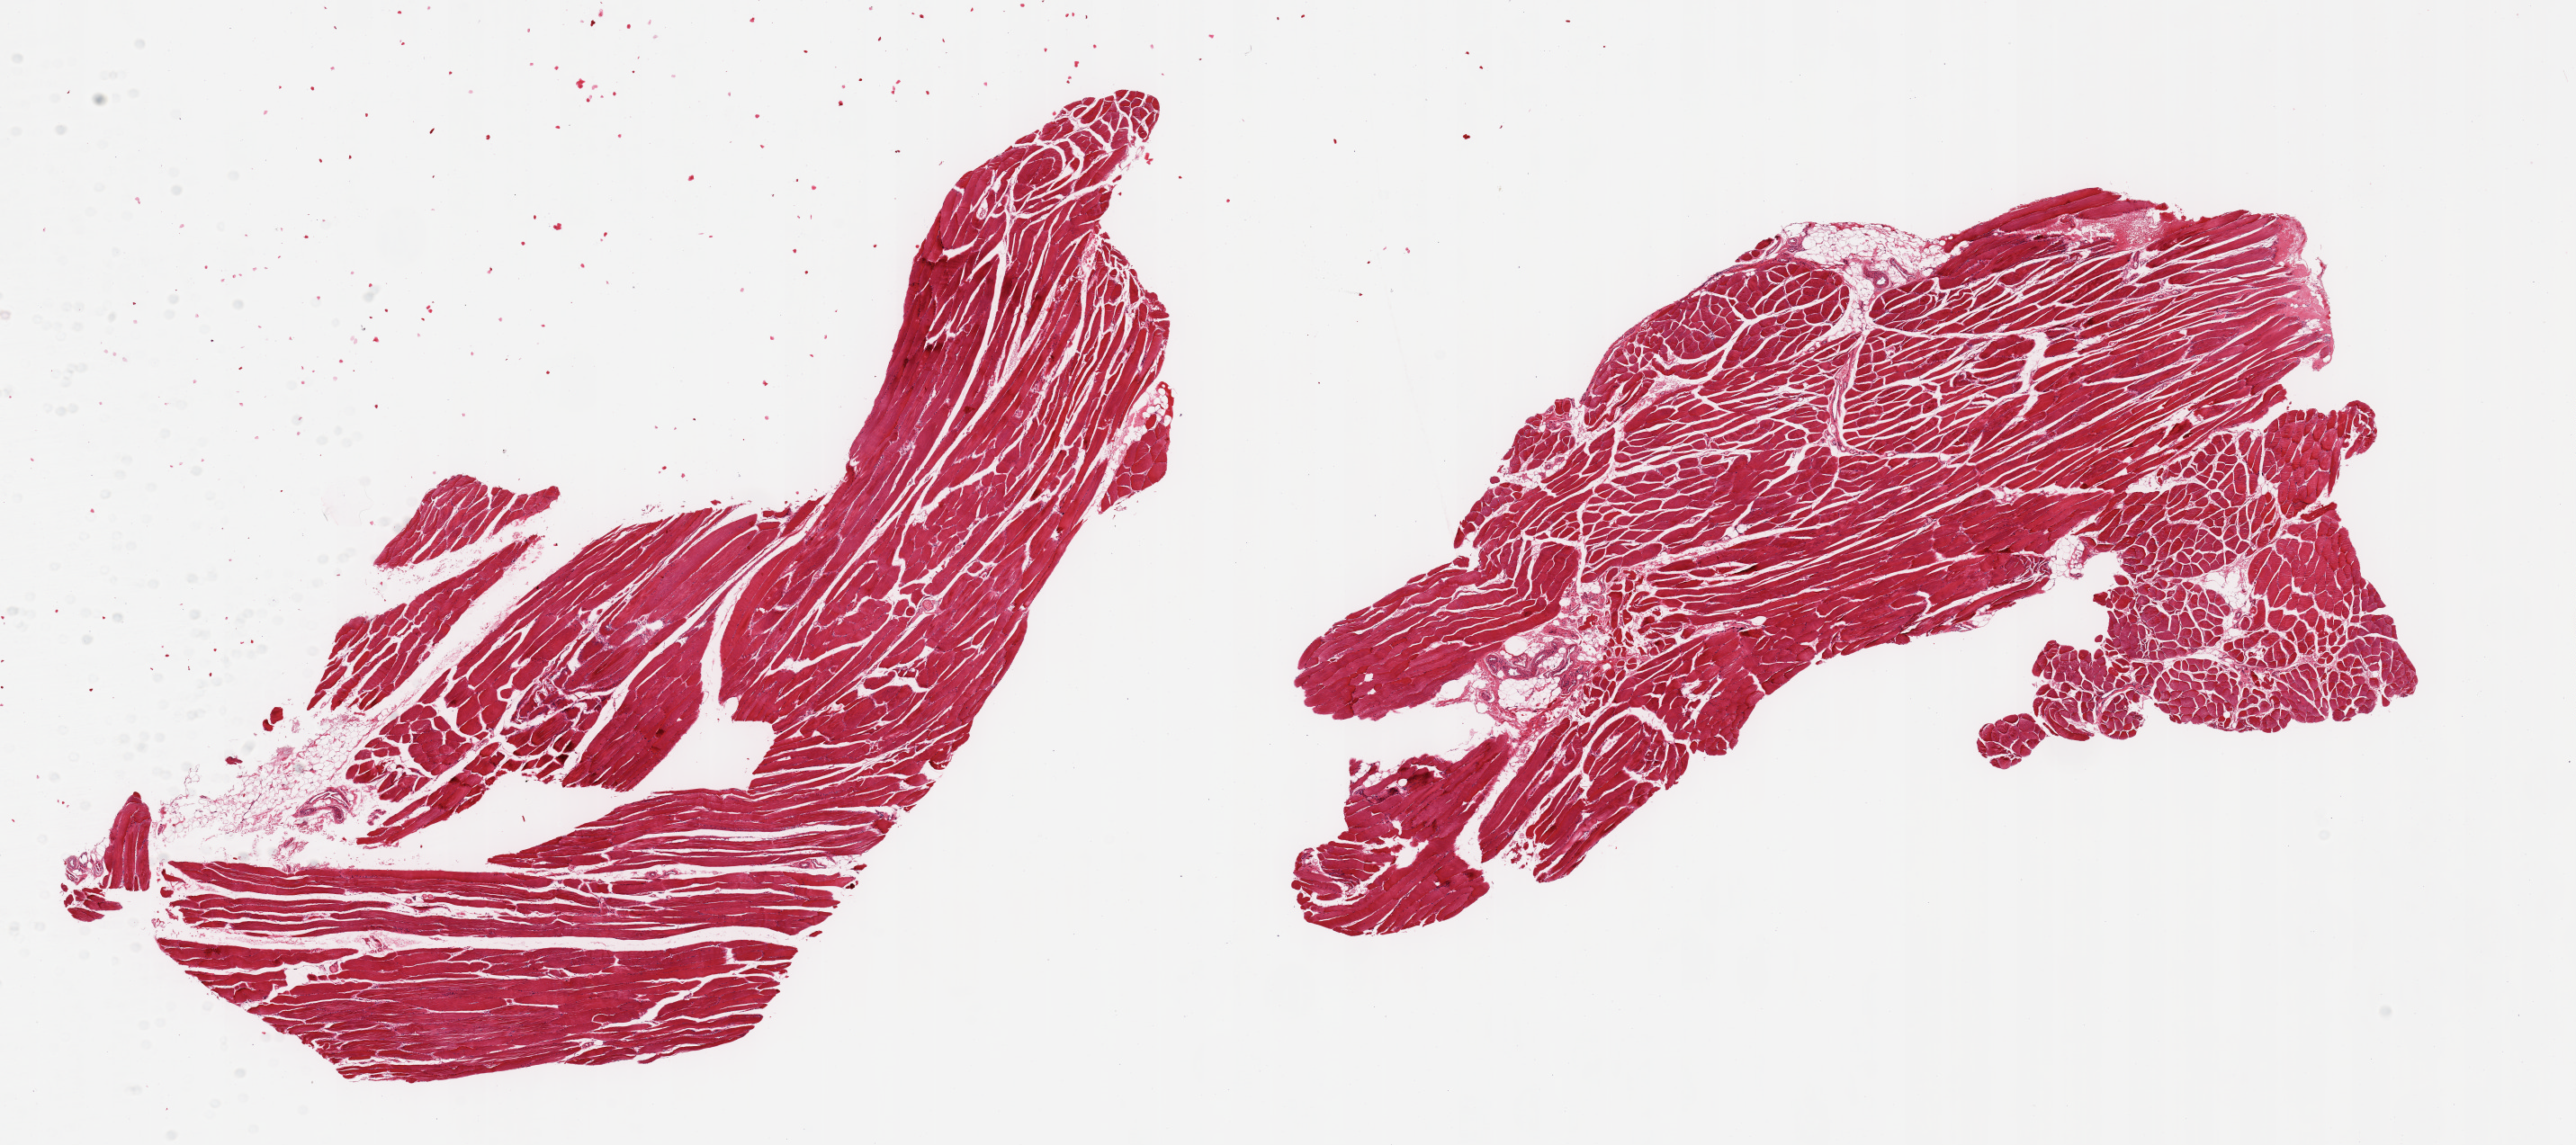
Hematoxylin and eosin (H&E) whole-slide image, low-resolution overview of the scanned area, about 22.6 x 10.1 mm; PAXgene-fixed paraffin-embedded (PFPE) section; target tissue: skeletal muscle; donor tissue sample.
Pathologist's review note for this sample: 2 pieces; ~5% internal fat.